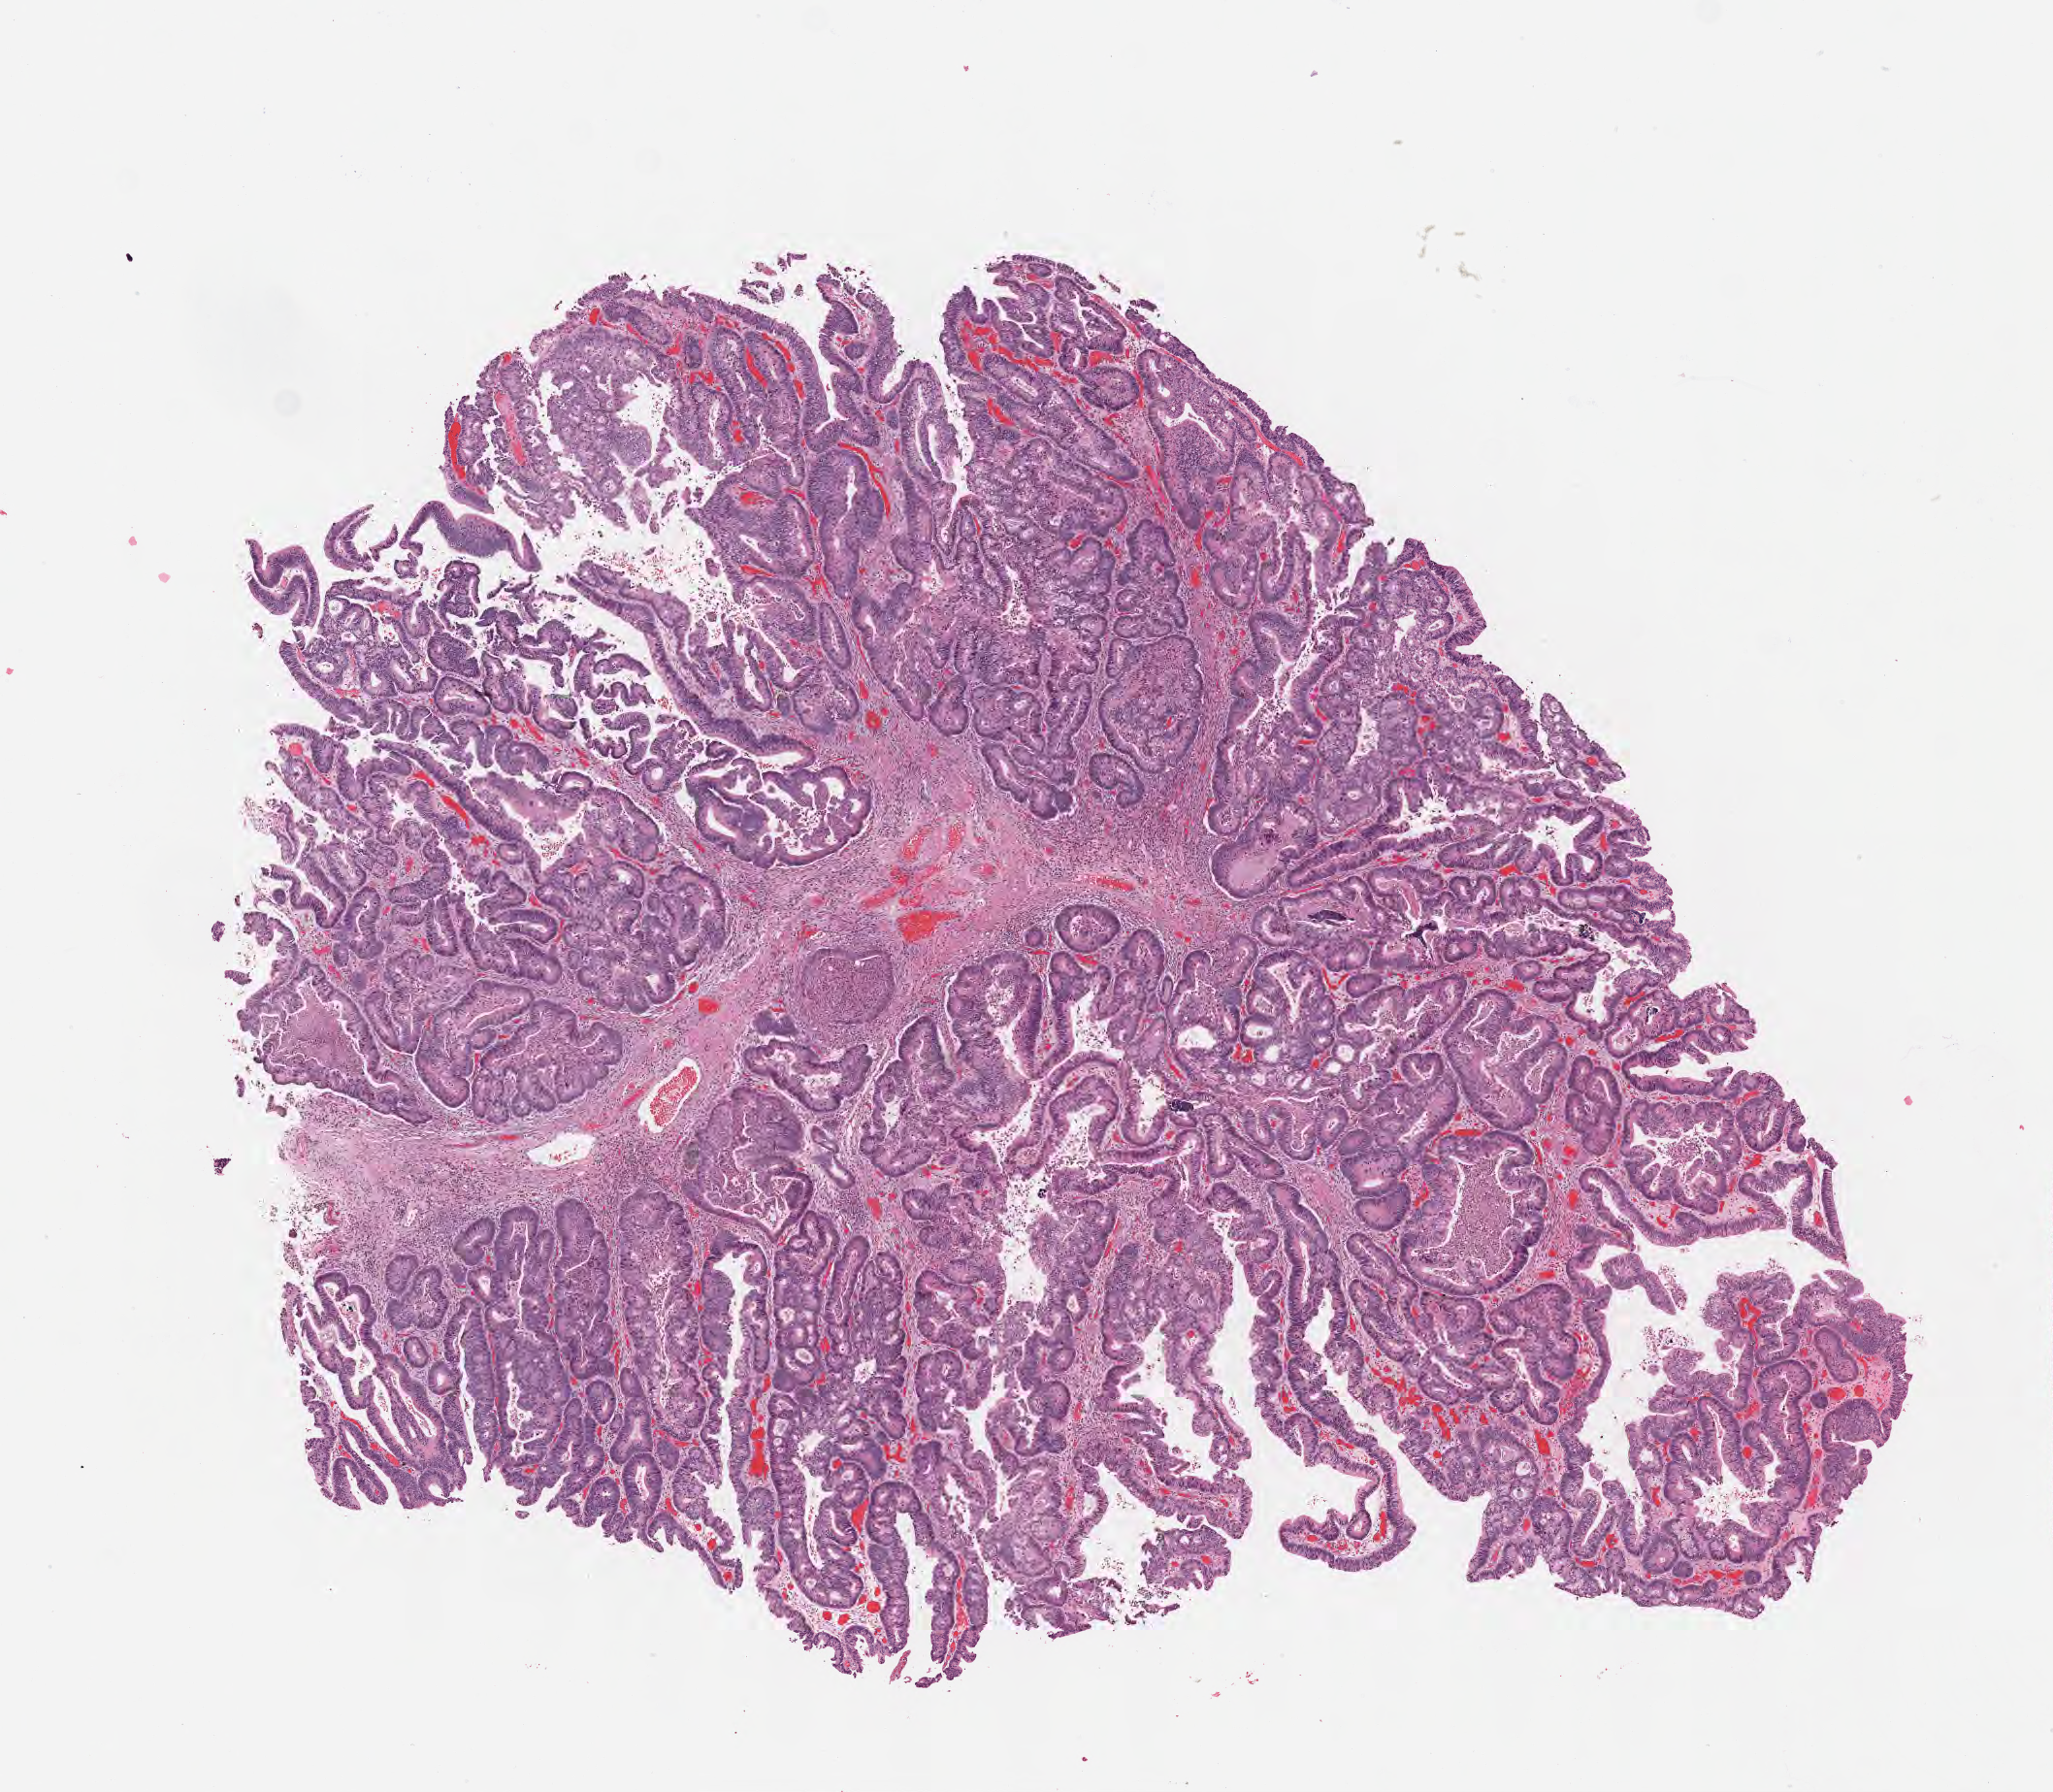
Digitized H&E-stained section — whole scanned area (about 8.6 x 7.5 mm) shown as a low-resolution overview, FFPE section, primary tumor, site: sigmoid colon. Patient: male, age at initial diagnosis 68 years. Tumor grade: GB (borderline). Pathologist review of this section (percent, as recorded): tumor cells 60%, tumor nuclei 60%, stromal cells 40%, necrosis 0%, normal cells 0%. Infiltration values recorded for this section: lymphocyte infiltration 0%, monocyte infiltration 0%, neutrophil infiltration 0%.
AJCC pathologic stage: Stage IVA. Diagnosis: Adenocarcinoma, NOS. Section: bottom of the tissue portion.